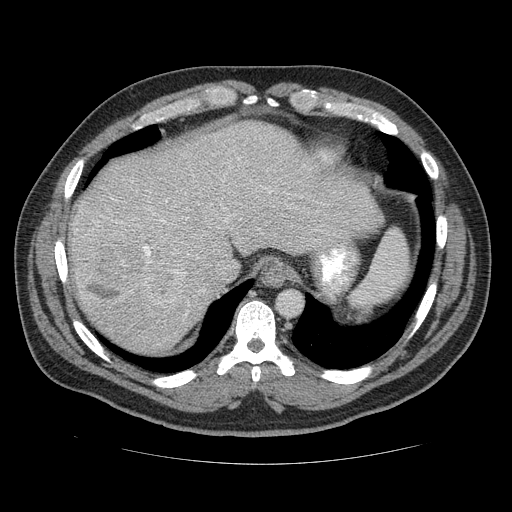
Contrast-enhanced abdominal CT (liver protocol), one axial slice. Position 99 of 113 along the scan axis. Soft-tissue window (W 400 / L 40 HU). 2.5 mm slice thickness. 512 × 512 image matrix, field of view 400 × 400 mm. From the clinical record (not read from this slice): diagnosis: hepatocellular carcinoma (patient treated with transarterial chemoembolisation; whether this scan precedes or follows treatment is not stated here); TNM stage (as recorded): Stage-II; Child-Pugh class: B; tumour differentiation: moderately differentiated; tumour size: 4.8 cm.
Structures marked on this image (semi-automatic segmentation, software-assisted and operator-edited):
- abdominal aorta: bounding box <279,292,301,315> (left, top, right, bottom; pixels)
- liver parenchyma outside the tumour (the mass and vessels are separate outlines, so this box may not span the whole liver): <68,124,384,352>
- mass: <70,213,179,304>
- liver vessels: <110,199,190,307>